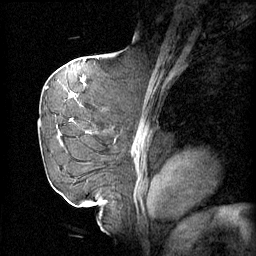
Breast MRI (dynamic contrast-enhanced), one sagittal slice. Slice 36 of 60 in the series (ordered by position). 4 images stored at this slice position (order not interpretable as contrast timing). 1.5 T. TE 4.2 ms, TR 11 ms. 2 mm slice thickness. 256 × 256 image matrix. Female patient, age 72 years.
Outlined on this slice (semi-automatic segmentation, software-assisted and operator-edited):
- analysis volume of interest (the breast-tissue region the enhancement analysis was run in; not a lesion): bounding box [x1, y1, x2, y2] px = [45, 68, 106, 163]
- tumour enhancement mask (voxels above the 70 % enhancement threshold inside the analysis volume of interest): [55, 68, 106, 127]